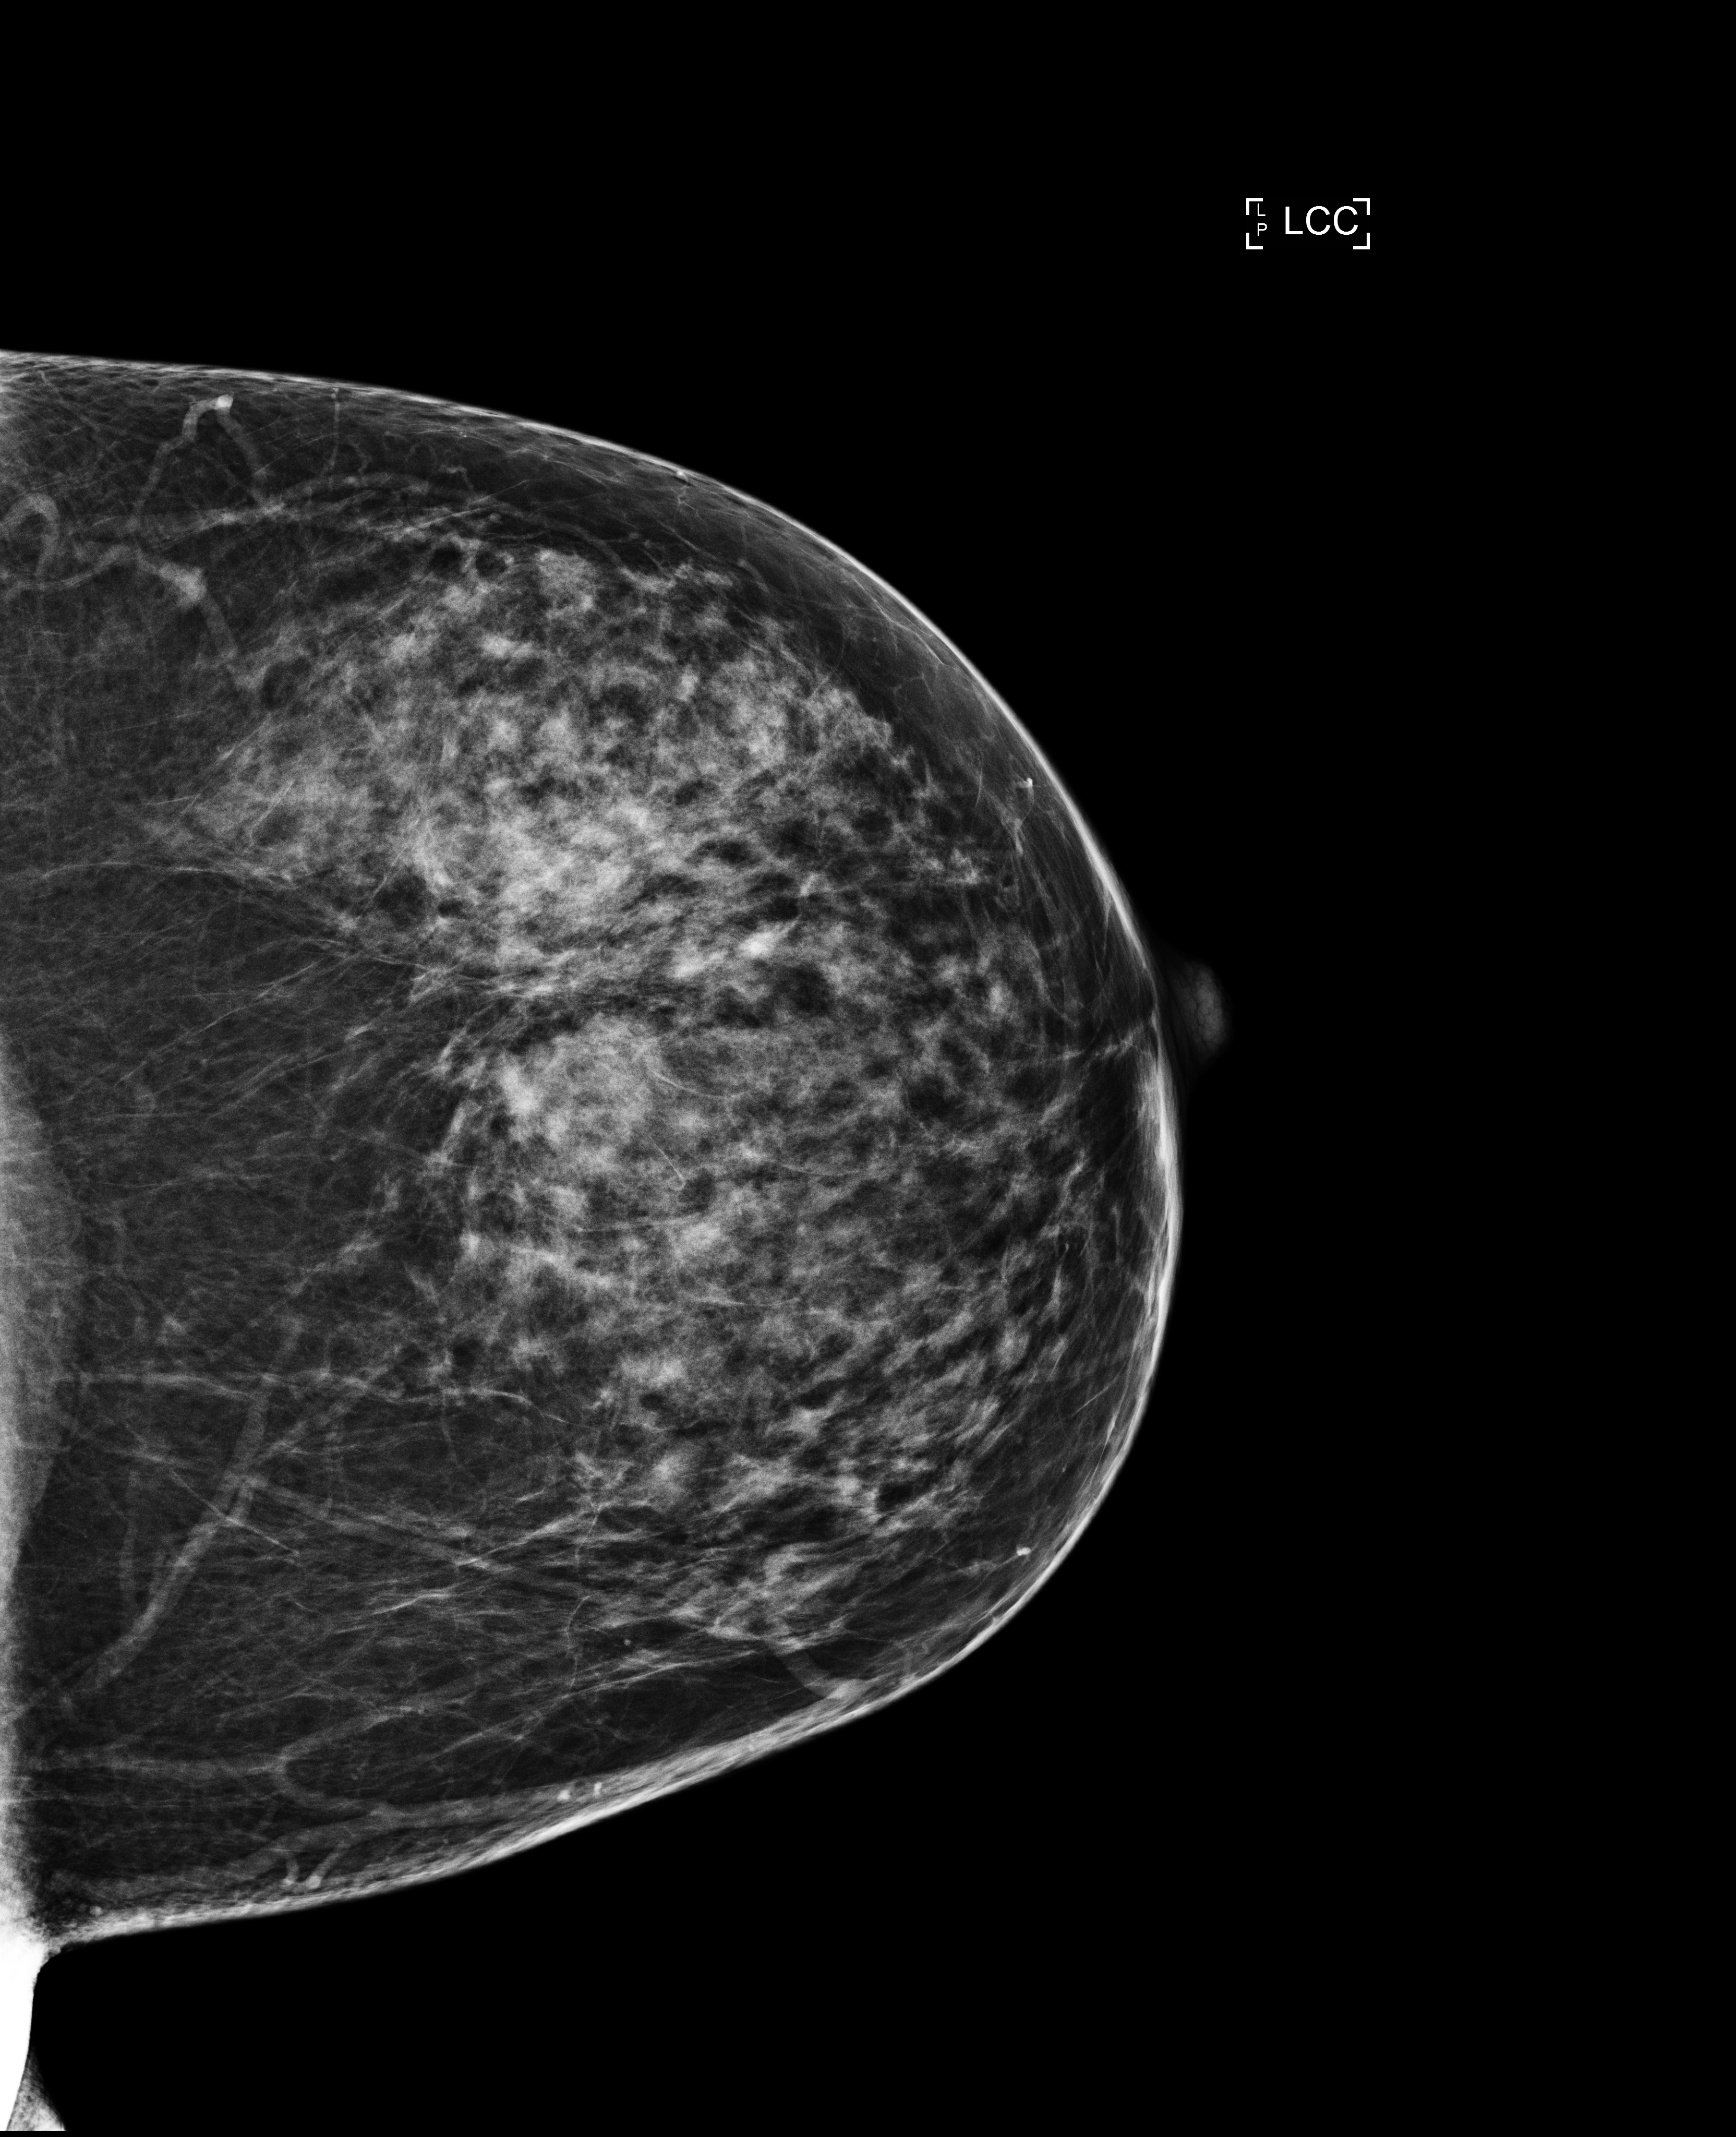
Full-field digital mammogram (FFDM), left breast, cranio-caudal projection, screening examination, compressed breast thickness 63 mm, system: Selenia Dimensions. Patient: female, 50 years.
- BI-RADS breast density category at the screening exam (both breasts, scale 1–4): 3
- final BI-RADS category for the screening round (tomosynthesis exam, both breasts): category 1
- recall: no recall after this screen